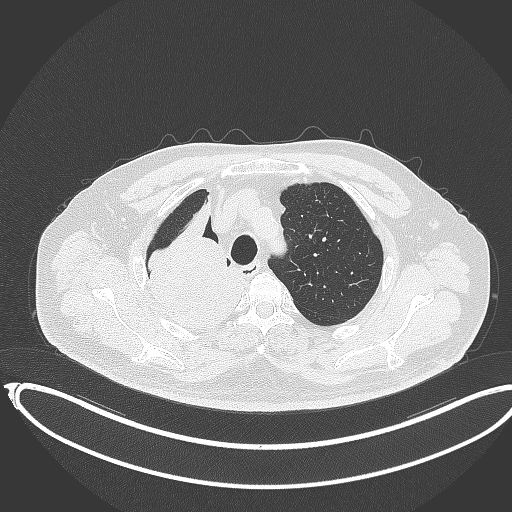
Chest CT, one axial slice. Slice 294 of 403 in the series (ordered by position). Reconstruction kernel B70f. Lung window (W 1500 / L -600 HU). 1 mm slice thickness. 512 × 512 image matrix, field of view 436 × 436 mm. Patient: male, 68 years. Case-level facts recorded for this patient, not image findings: clinical TNM (as recorded): T2a N0 M0.
Annotated regions visible in this slice (rectangle marked by the reading radiologist):
- lung tumour (recorded histology: adenocarcinoma): bounding box <137,195,248,331> (left, top, right, bottom; pixels)